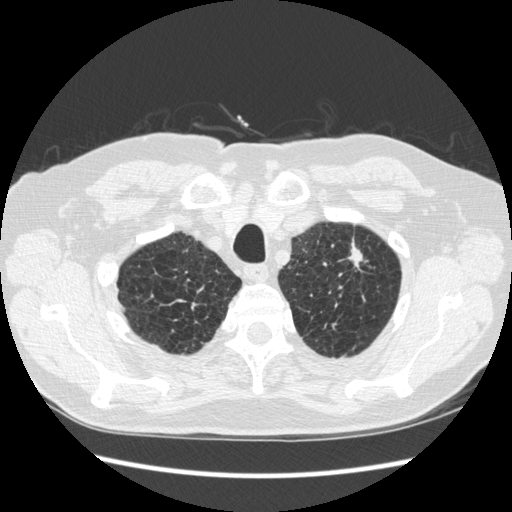
Axial slice from a low-dose chest CT screening exam; third screening round (two years after baseline); lung window (W 1500 / L -600 HU); 1.25 mm slice thickness; standard (soft-tissue) reconstruction kernel (STANDARD); 120 kVp. Male, age 70 years at enrolment. Former smoker at enrolment.
- Expert reader's lesion annotation, bounding box <324,230,378,295> (left, top, right, bottom; pixels).
- The screening reader recorded 2 non-calcified nodules or masses ≥4 mm on this exam (left upper lobe, right lower lobe); which of them this box marks is not recorded.
- Official screen result: positive, other.
- Later outcome: lung cancer diagnosed 92 days after this screen — squamous cell carcinoma, NOS, left upper lobe, moderately differentiated (G2), stage IA (AJCC 6th edition), 18 mm at pathology.